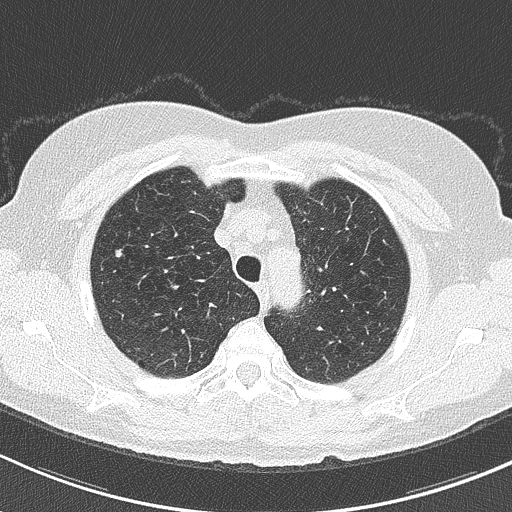
Low-dose screening chest CT, axial slice; first (baseline) screen; lung window (W 1500 / L -600 HU); 120 kVp. Female, age 60 years at enrolment.
• Lesion marked by an expert reader, bounding box (x1, y1, x2, y2) in pixels: (104, 239, 133, 269).
• Screening reader's record for this exam (one nodule recorded; not confirmed to be the boxed lesion): non-calcified nodule or mass ≥4 mm, right upper lobe, 4 × 4 mm, smooth margins, soft tissue attenuation.
• Lung cancer was diagnosed 216 days after this screen: acinar cell carcinoma, right upper lobe, well differentiated (G1), stage IA (AJCC 6th edition), 7 mm at pathology.